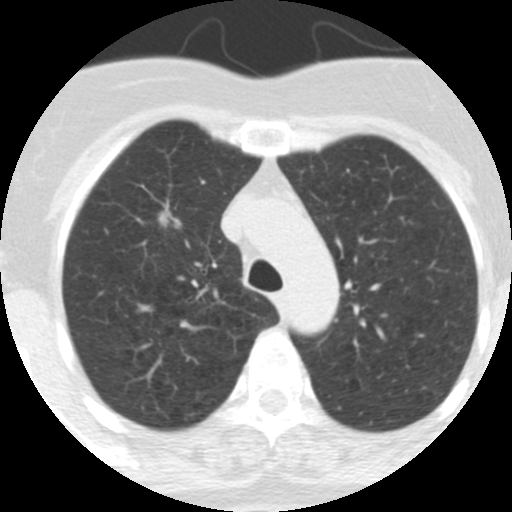
Low-dose screening chest CT, one axial slice. Position 237 of 313 along the scan axis. Reconstruction kernel STANDARD. Lung window (W 1500 / L -600 HU). 2.5 mm slice thickness. 512 × 512 image matrix, field of view 253 × 253 mm.
Annotated regions visible in this slice (outlined manually by an expert reader):
- lesion 1 (tumor, upper lobe of right lung): bounding box <159,211,181,228> (left, top, right, bottom; pixels)